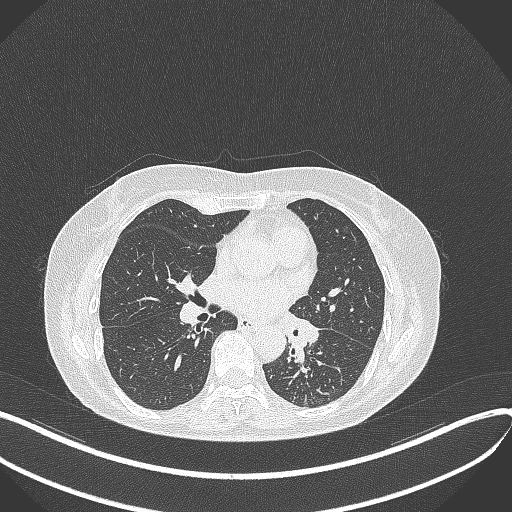
Chest CT, one axial slice; slice 209 of 429 in the series (ordered by position); reconstruction kernel B70f; lung window (W 1500 / L -600 HU); 1 mm slice thickness; 512 × 512 image matrix. Patient: female, 63 years. From the clinical record (not read from this slice): clinical TNM (as recorded): T1b N0 M0; histopathological grade: G2-3.
Annotated regions visible in this slice (rectangle marked by the reading radiologist):
- lung tumour (recorded histology: adenocarcinoma): bounding box (x1, y1, x2, y2) in pixels: (283, 314, 320, 365)